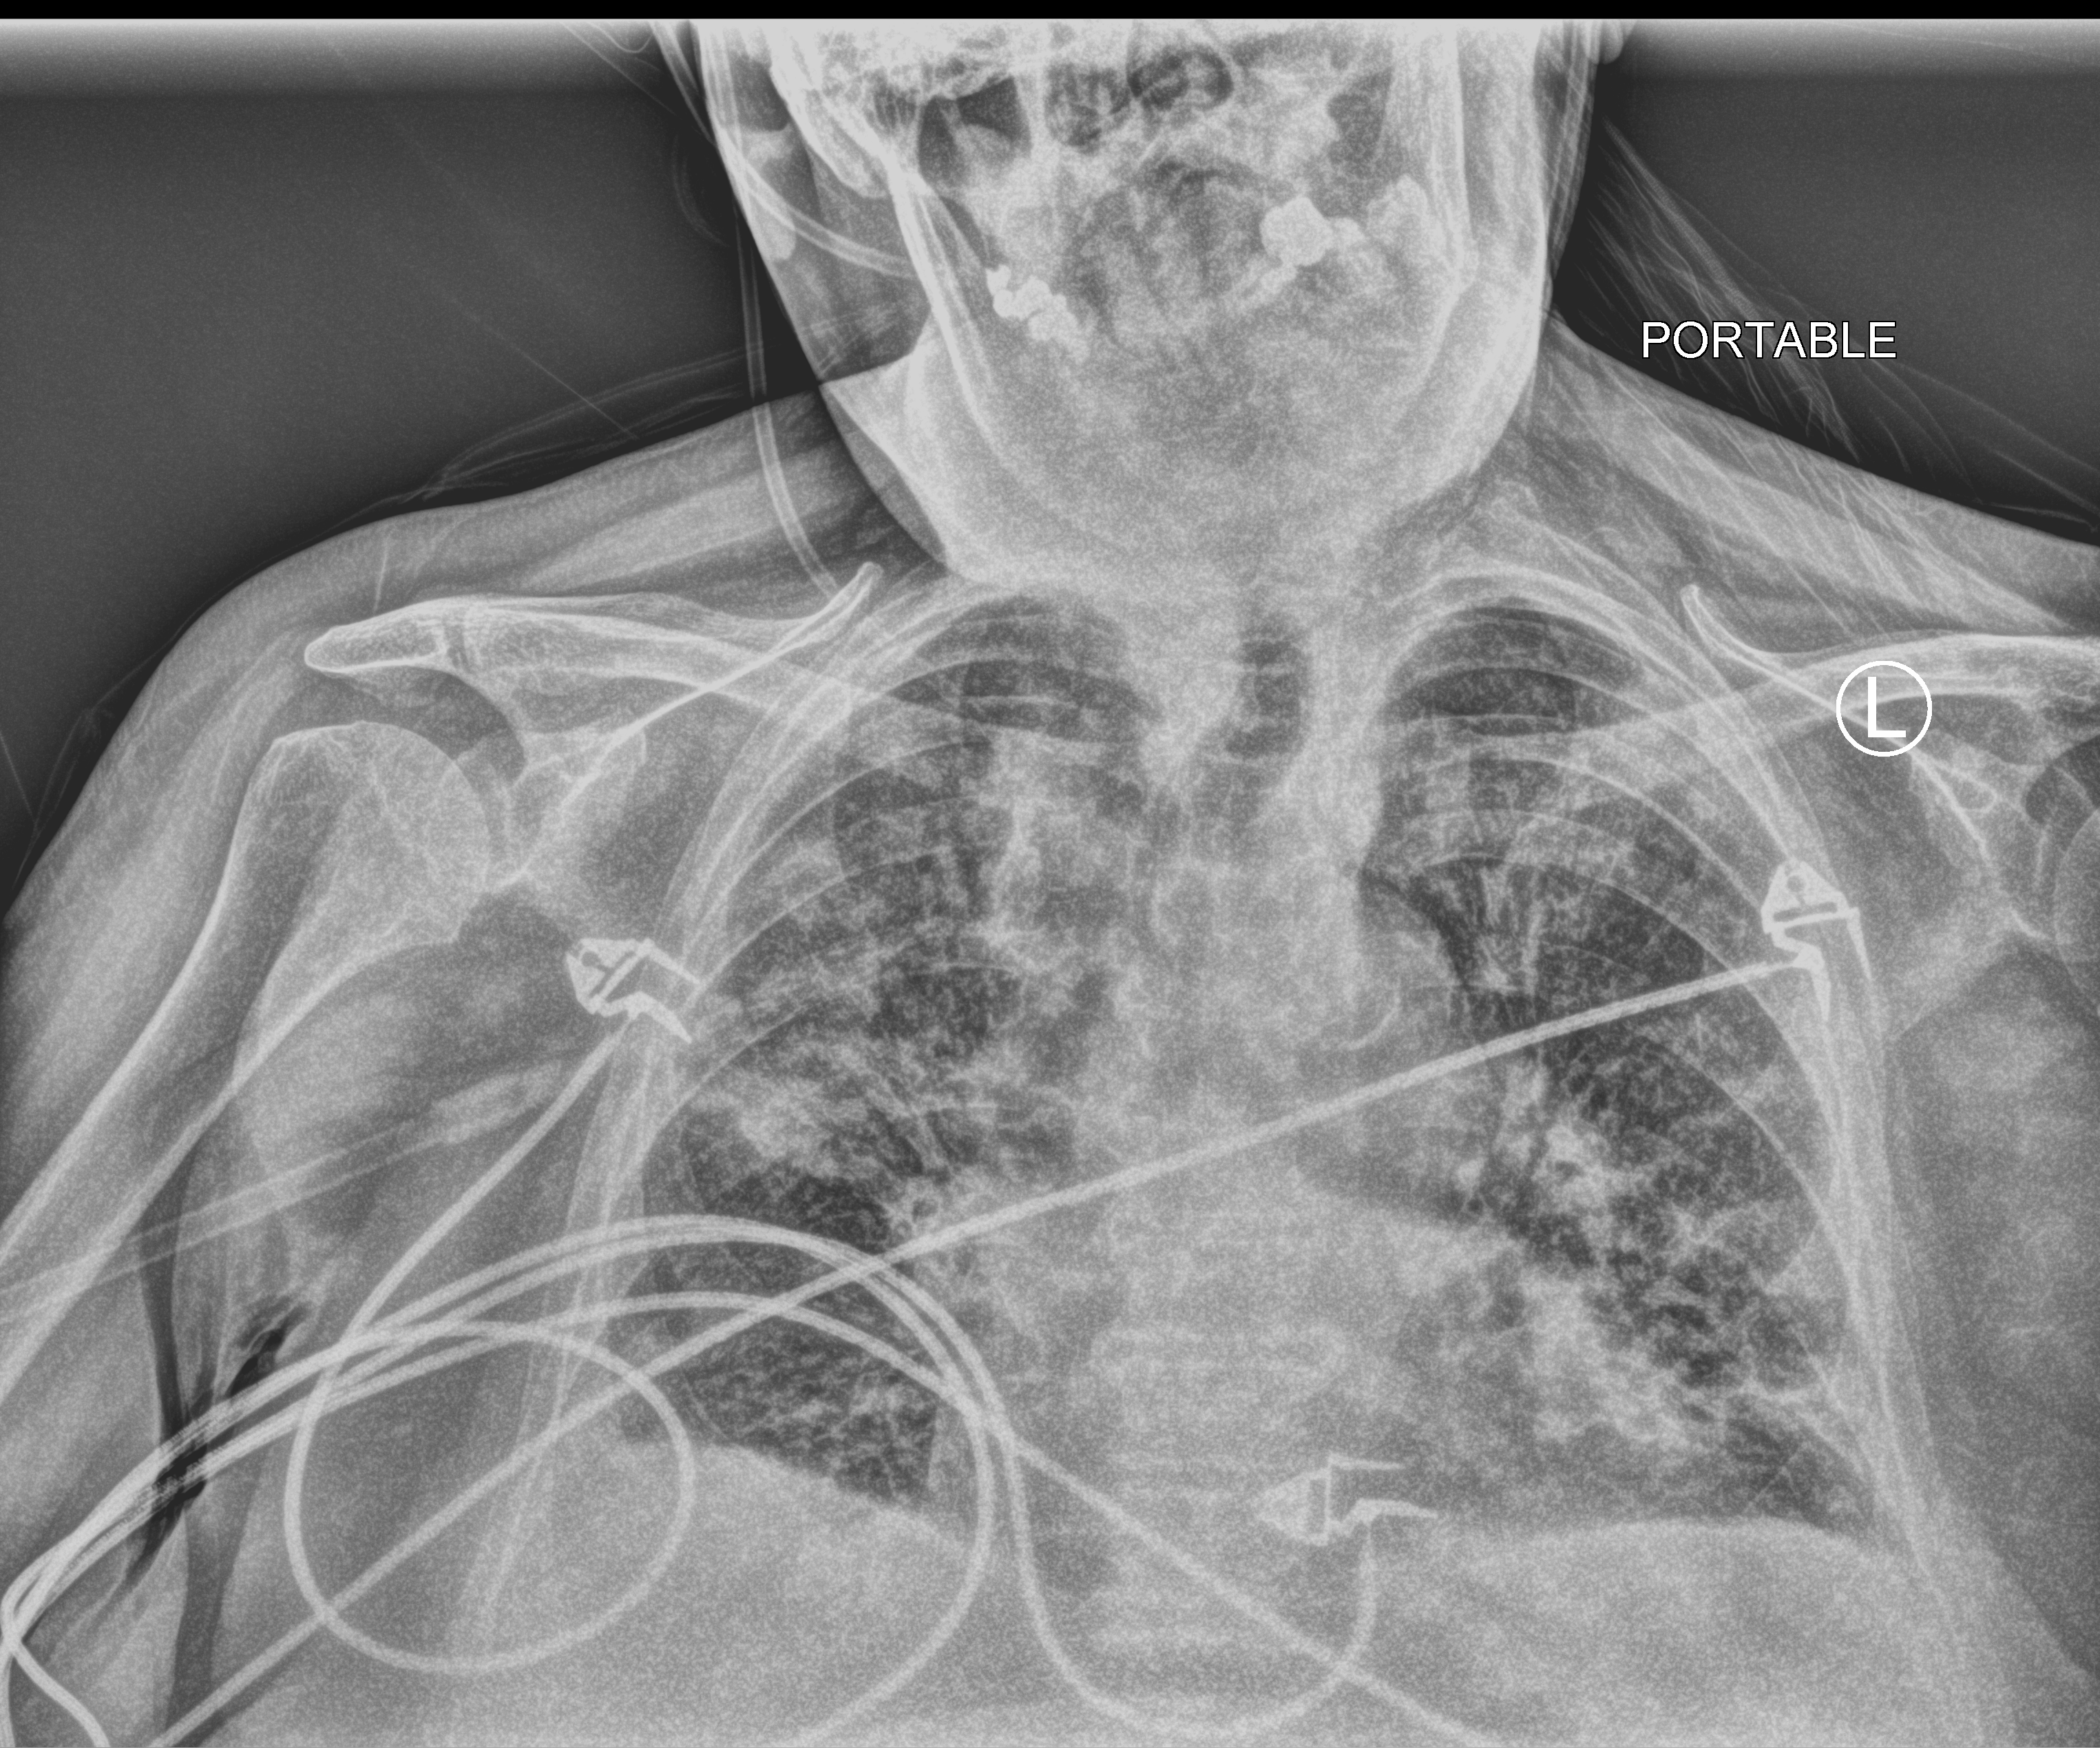
Portable chest radiograph. Female patient hospitalised with COVID-19, age 75–90 years.
Hospital-stay facts (about this admission, not read from this image; timing relative to this image not recorded): admitted to intensive care during this hospital stay: no; hypertension (admission record): no.